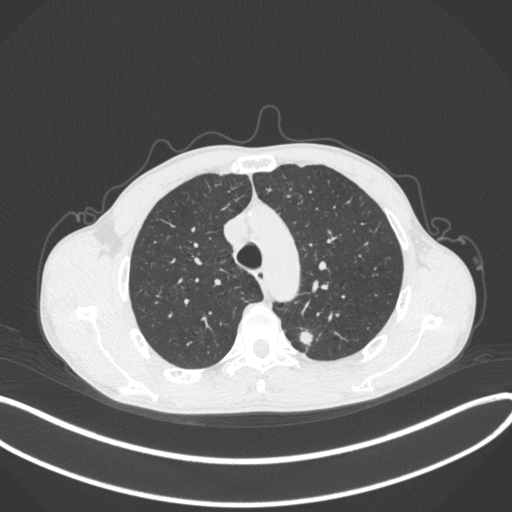
Chest CT, one axial slice; position 301 of 429 along the scan axis; reconstruction kernel B31f; lung window (W 1500 / L -600 HU); 512 × 512 image matrix. Male patient, age 51 years. From the clinical record (not read from this slice): clinical TNM (as recorded): T2a N1 M1.
Outlined on this slice (rectangle marked by the reading radiologist):
- lung tumour (recorded histology: adenocarcinoma): box from (x=295, y=327) to (x=318, y=352) px